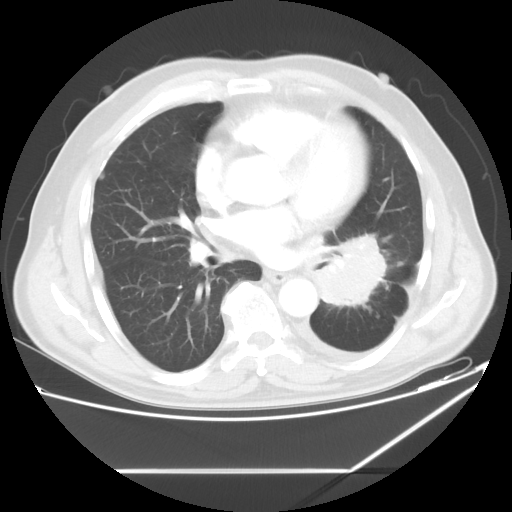
Chest CT, one axial slice. Position 29 of 60 along the scan axis. 120 kVp. Lung window (W 1500 / L -600 HU). 5 mm slice thickness. 512 × 512 image matrix. Patient: male, 62 years. Case-level facts recorded for this patient, not image findings: clinical TNM (as recorded): T3 N0 M1.
Outlined on this slice (rectangle marked by the reading radiologist):
- lung tumour (recorded histology: adenocarcinoma): box from (x=310, y=232) to (x=391, y=311) px
- lung tumour (recorded histology: adenocarcinoma): (x=313, y=236)–(x=384, y=308)